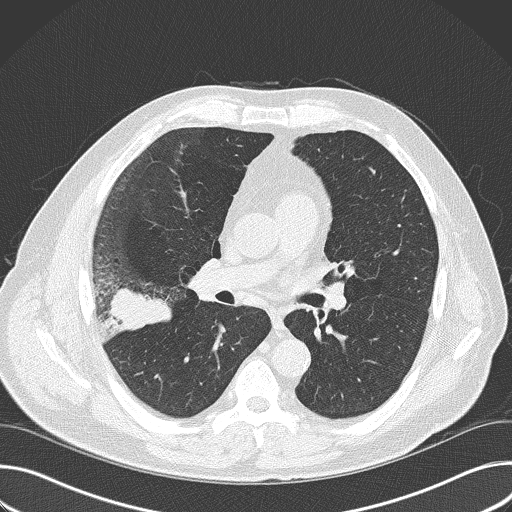
Low-dose screening chest CT, axial slice. First (baseline) screen. Lung window (W 1500 / L -600 HU). 2 mm slice thickness. Lung (sharp) reconstruction kernel (B50f). Male, age 56 years at enrolment. Current smoker at enrolment.
Lesion marked by an expert reader, bounding box [x1, y1, x2, y2] px = [79, 255, 182, 357]. The exam's reader record, not a measurement of the box and not confirmed to be the same lesion: non-calcified nodule or mass ≥4 mm, right upper lobe, 6 × 5 mm, spiculated (stellate) margins, soft tissue attenuation. Later outcome: lung cancer diagnosed 16 days after this screen — adenocarcinoma, NOS, right upper lobe, poorly differentiated (G3), stage IIB (AJCC 6th edition), 60 mm at pathology.